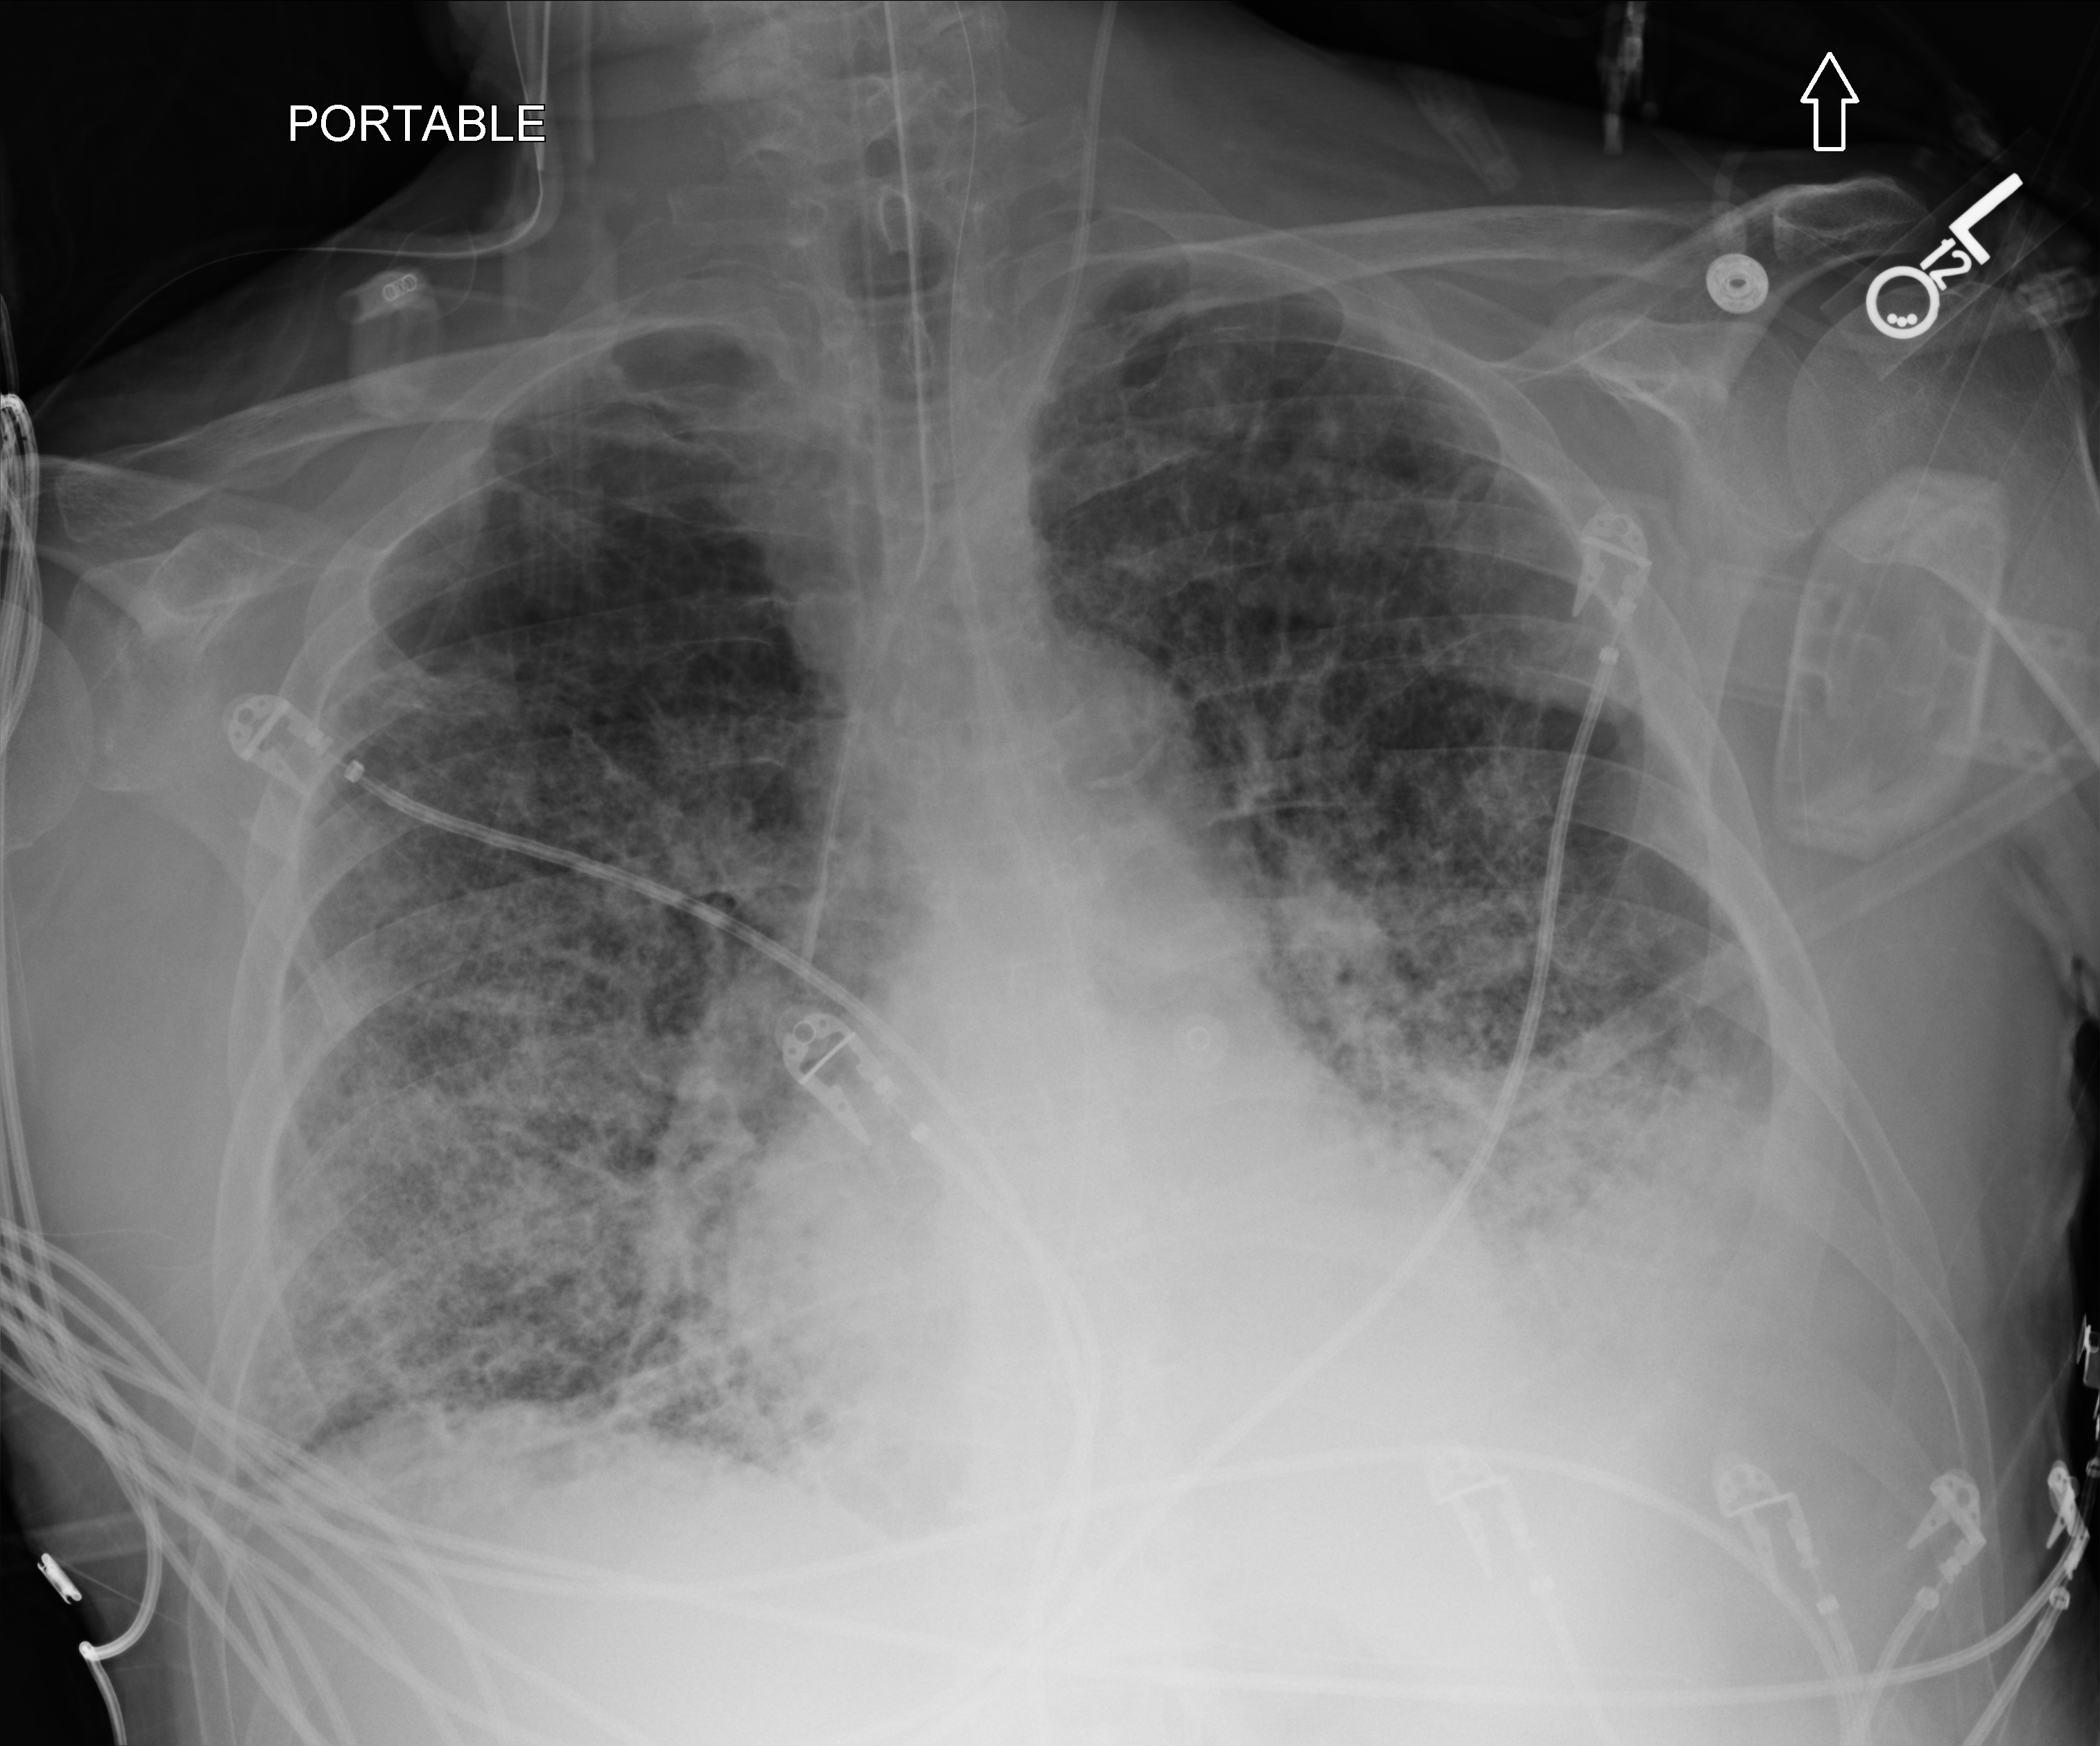
Portable chest radiograph; anteroposterior (AP) projection. Male patient hospitalised with COVID-19, age 75–90 years.
From the hospital-stay record, not from the radiograph (when in the stay this image was taken is not recorded):
- COPD (admission record): no